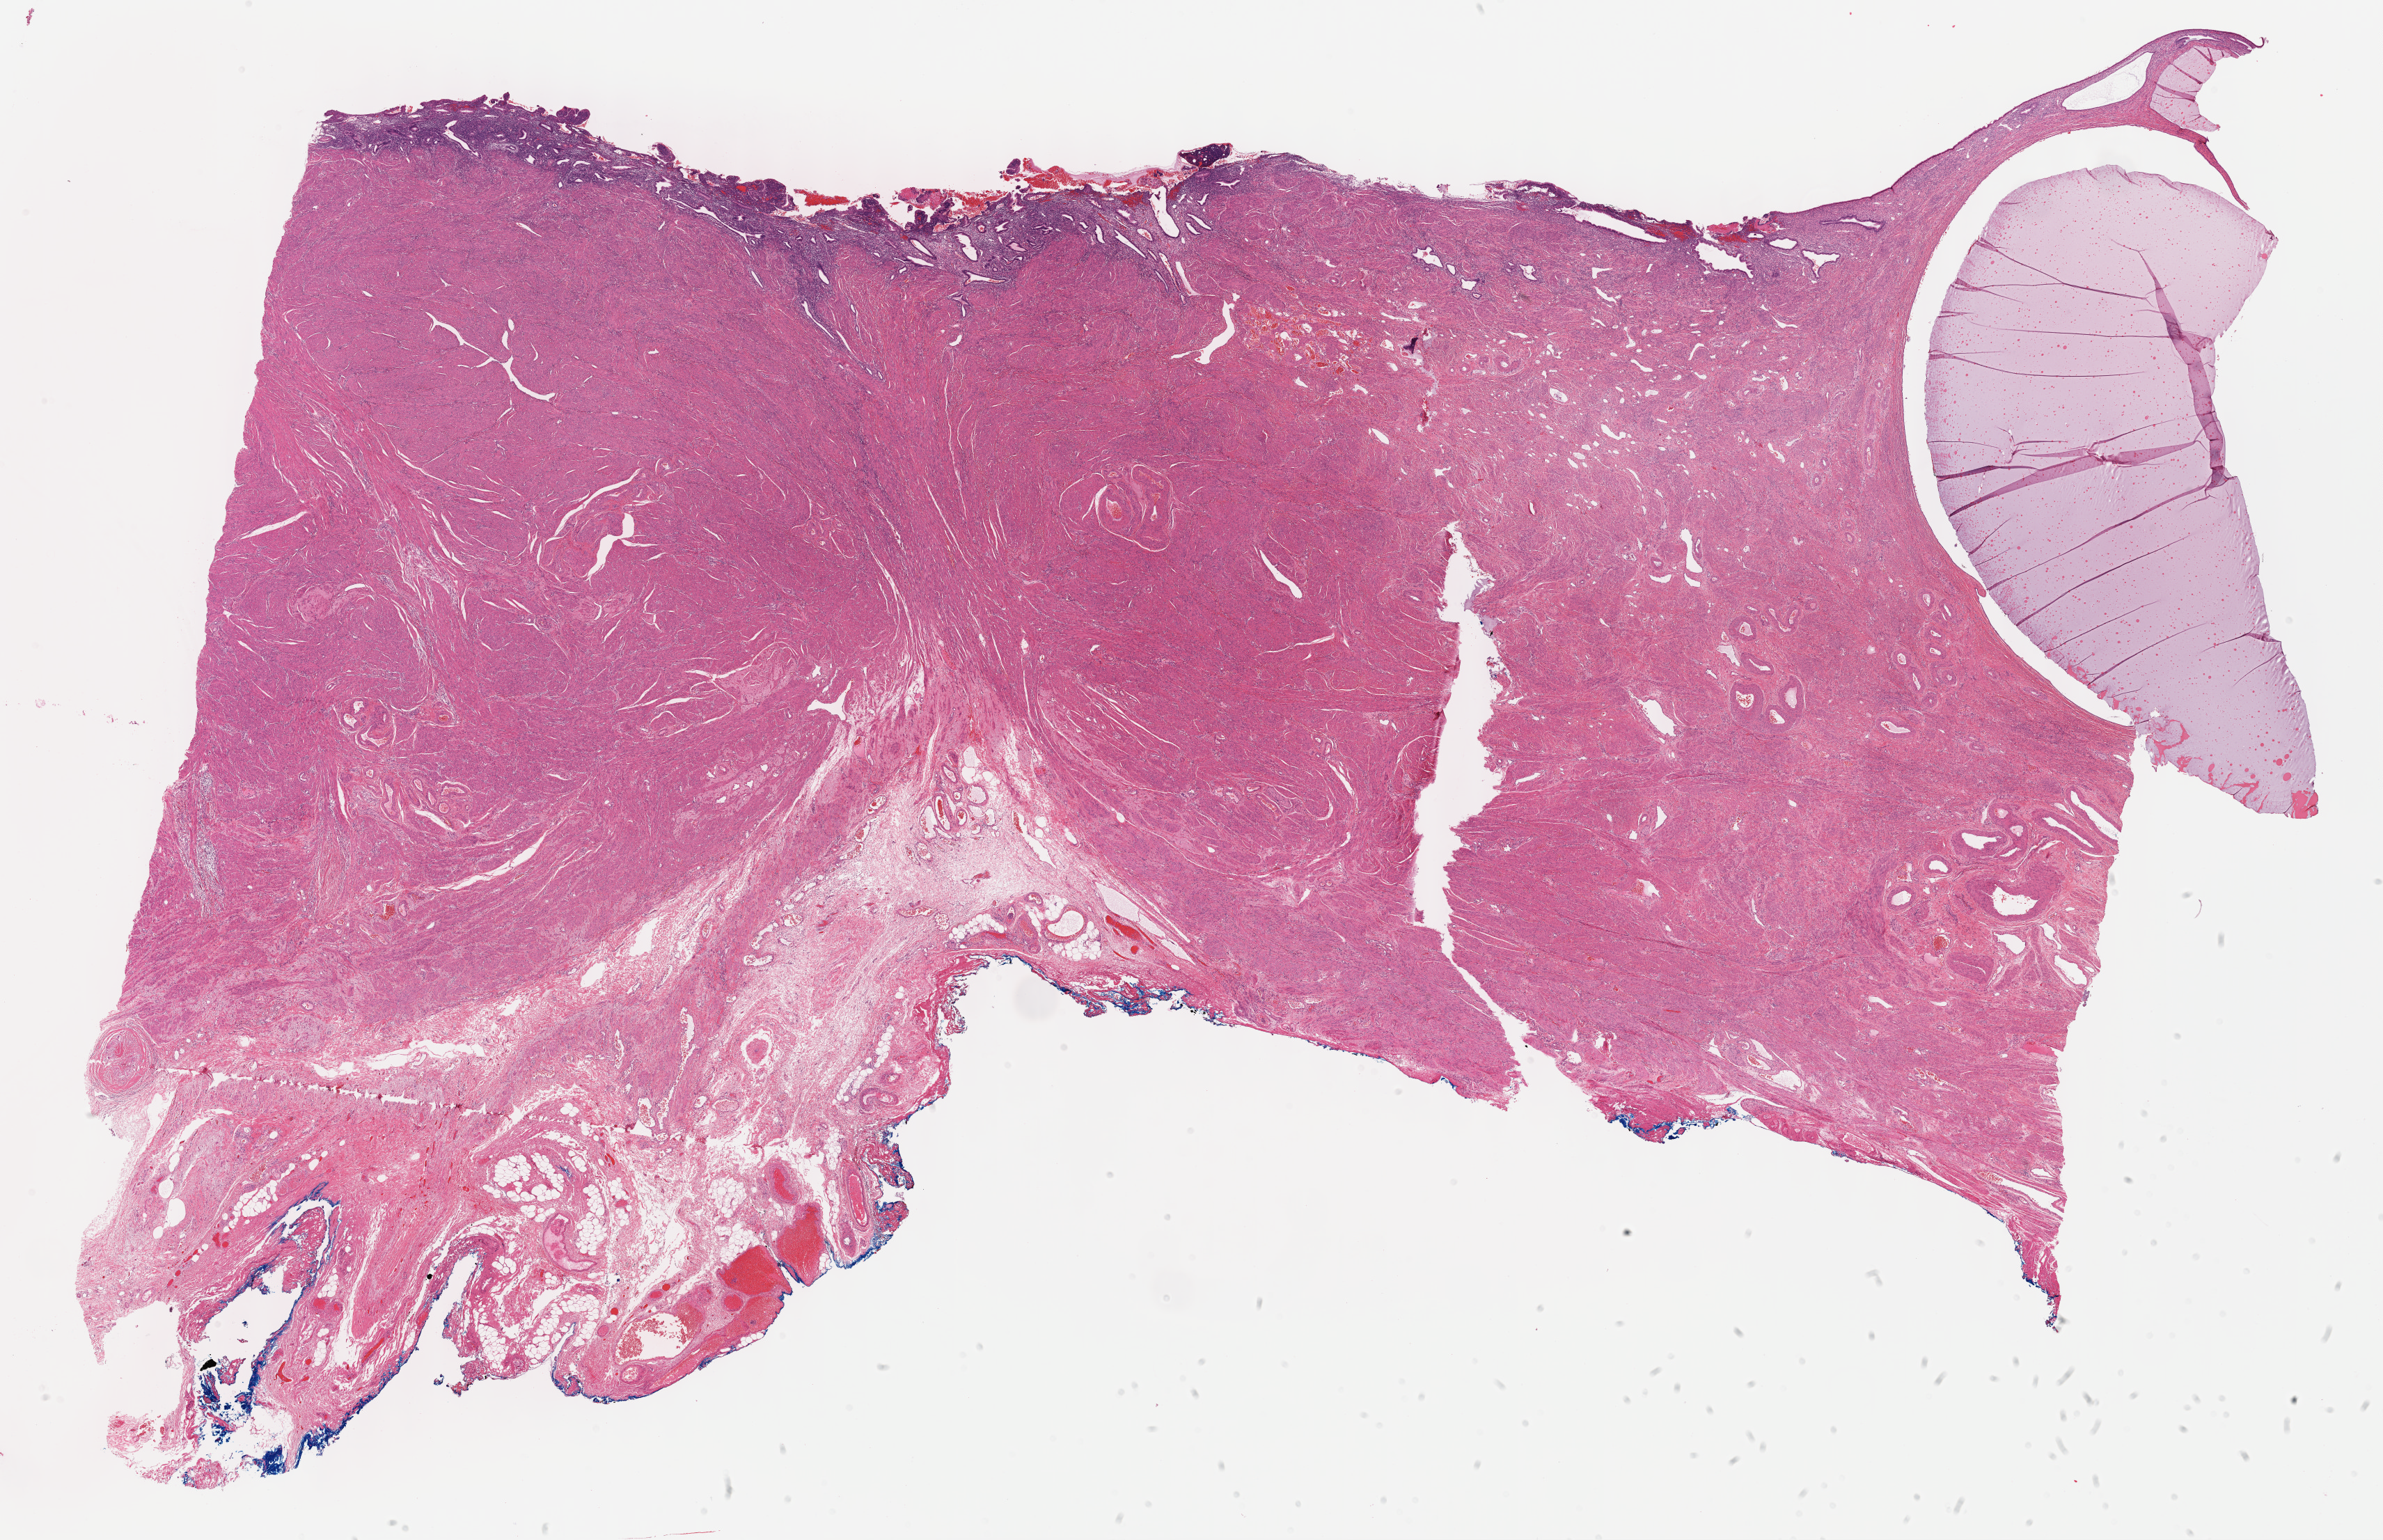
H&E whole-slide image, a low-resolution overview of the entire scanned area, about 27.7 x 17.9 mm (acquisition: 40x scan), formalin-fixed paraffin-embedded (FFPE) diagnostic section, cervix, primary tumour sample. Female, age 43 years at initial diagnosis. Histologic grade: G2 (moderately differentiated).
- FIGO stage: IIA2
- histologic diagnosis: Squamous cell carcinoma, large cell, nonkeratinizing, NOS (cervix uteri)